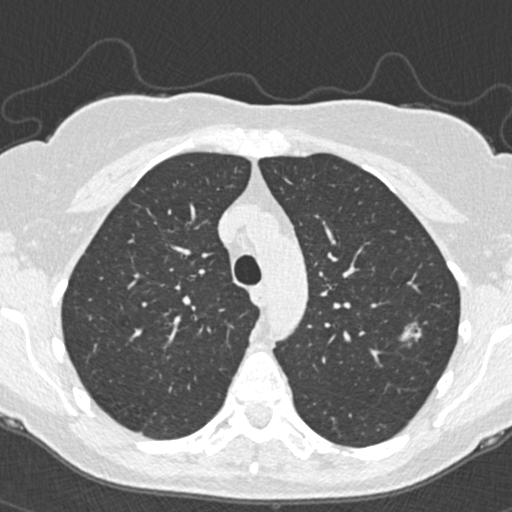
Low-dose screening chest CT, one axial slice; slice 266 of 350 in the series (ordered by position); lung window (W 1500 / L -600 HU); 1 mm slice thickness; 512 × 512 image matrix, field of view 298 × 298 mm.
Annotated regions visible in this slice (manually delineated by an expert):
- lesion 1 (tumor, upper lobe of left lung): bounding box [x1, y1, x2, y2] px = [400, 322, 422, 341]